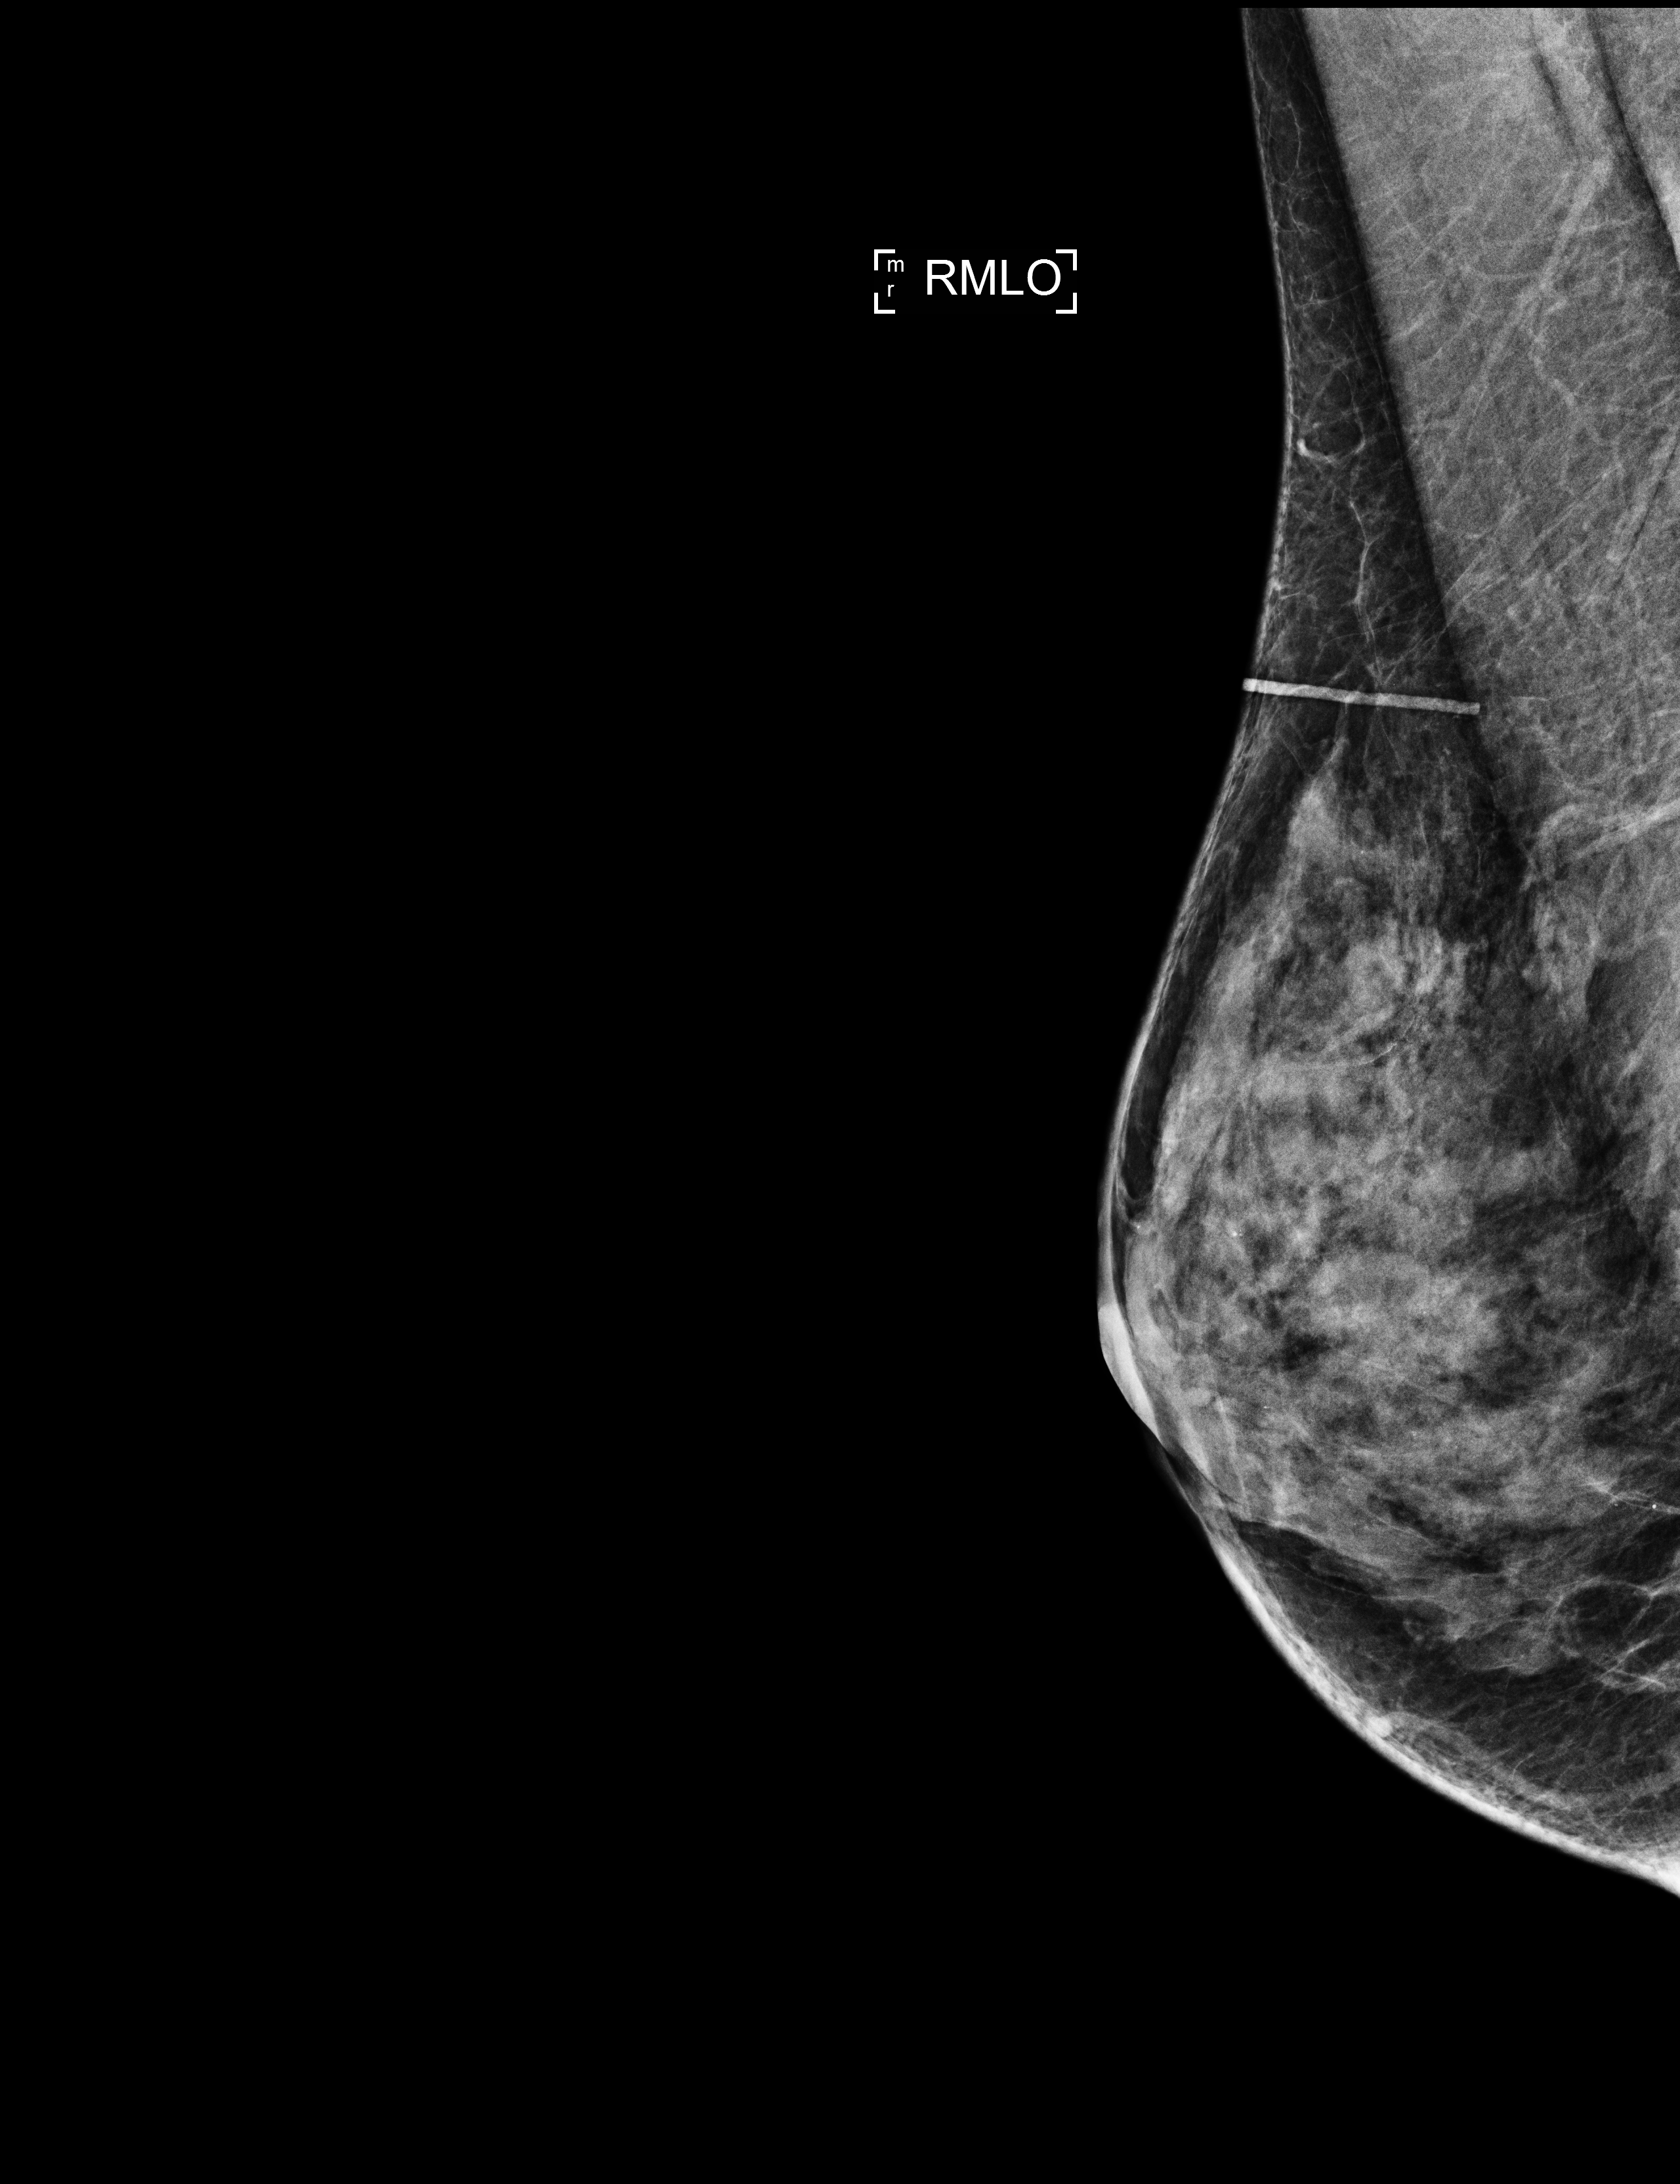
Screening examination. Patient aged 51 years (female).
Image type: full-field digital mammogram. Breast: right. Projection: medio-lateral oblique projection.